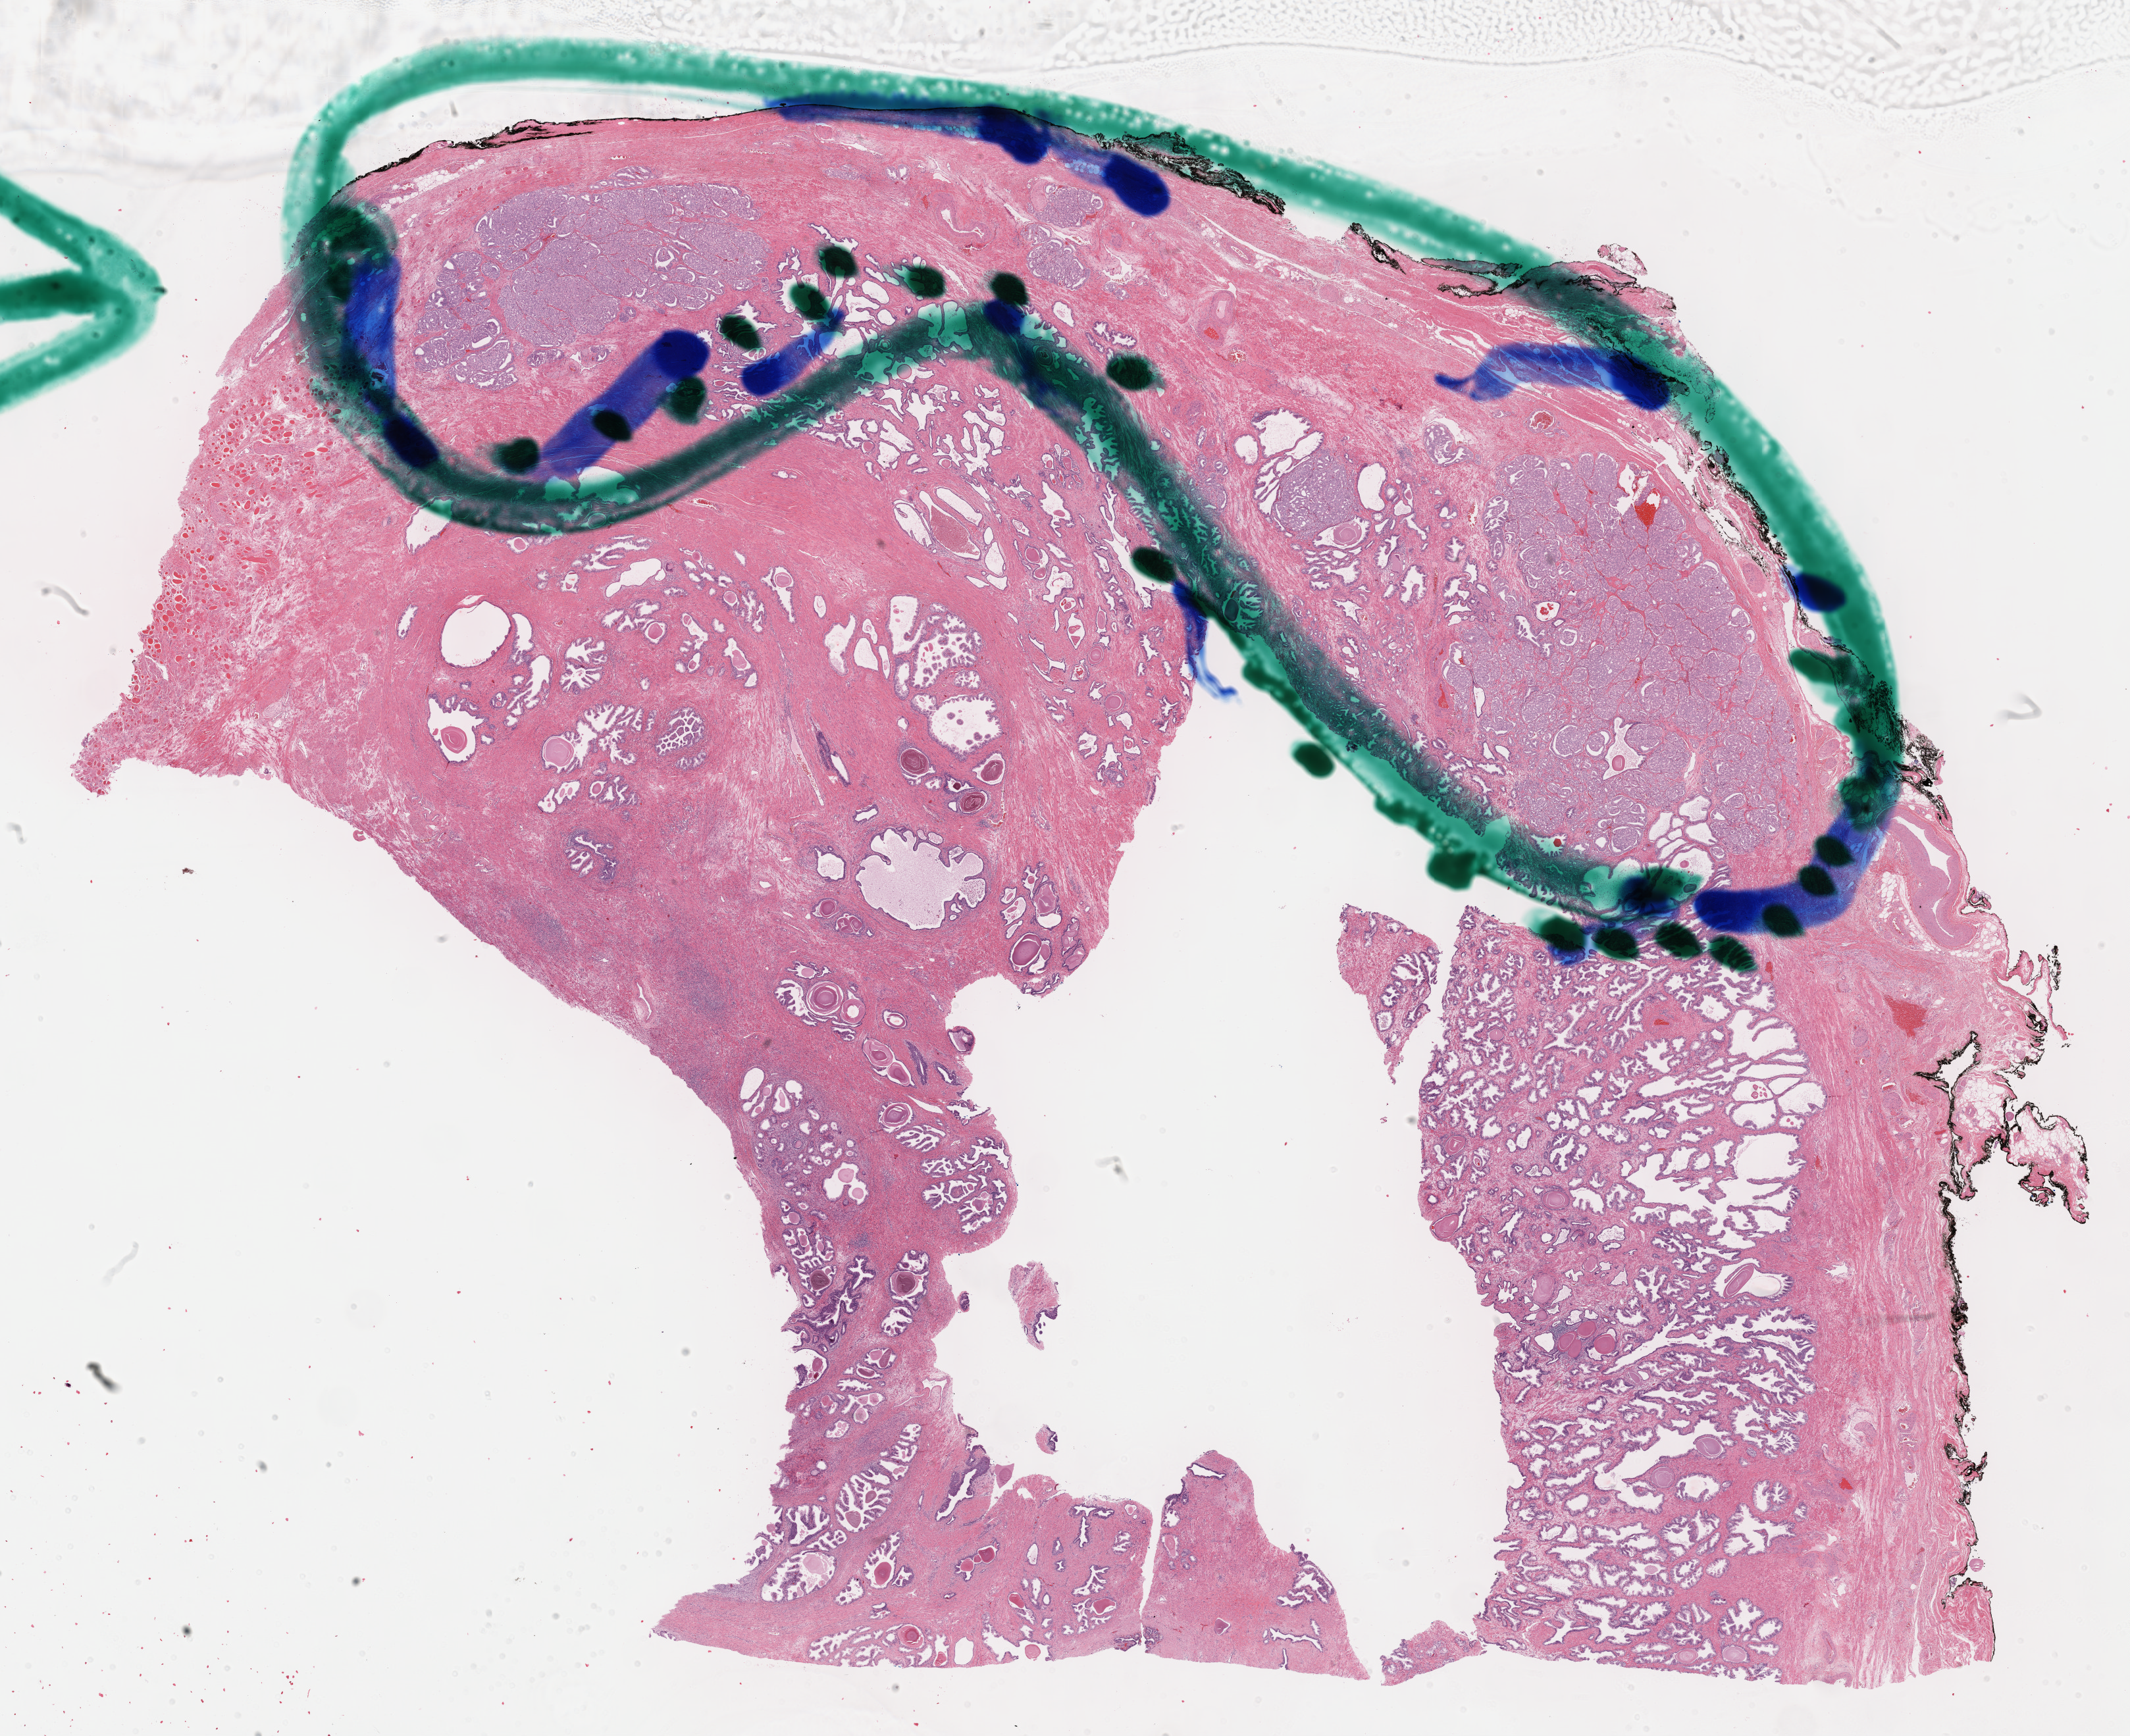
H&E-stained whole-slide image, shown as a low-resolution overview of the whole scanned area (about 26.2 x 21.3 mm). FFPE section. Primary tumour sample from the prostate. Male patient; age at initial diagnosis 65 years.
Diagnosis: Adenocarcinoma, NOS (prostate gland).